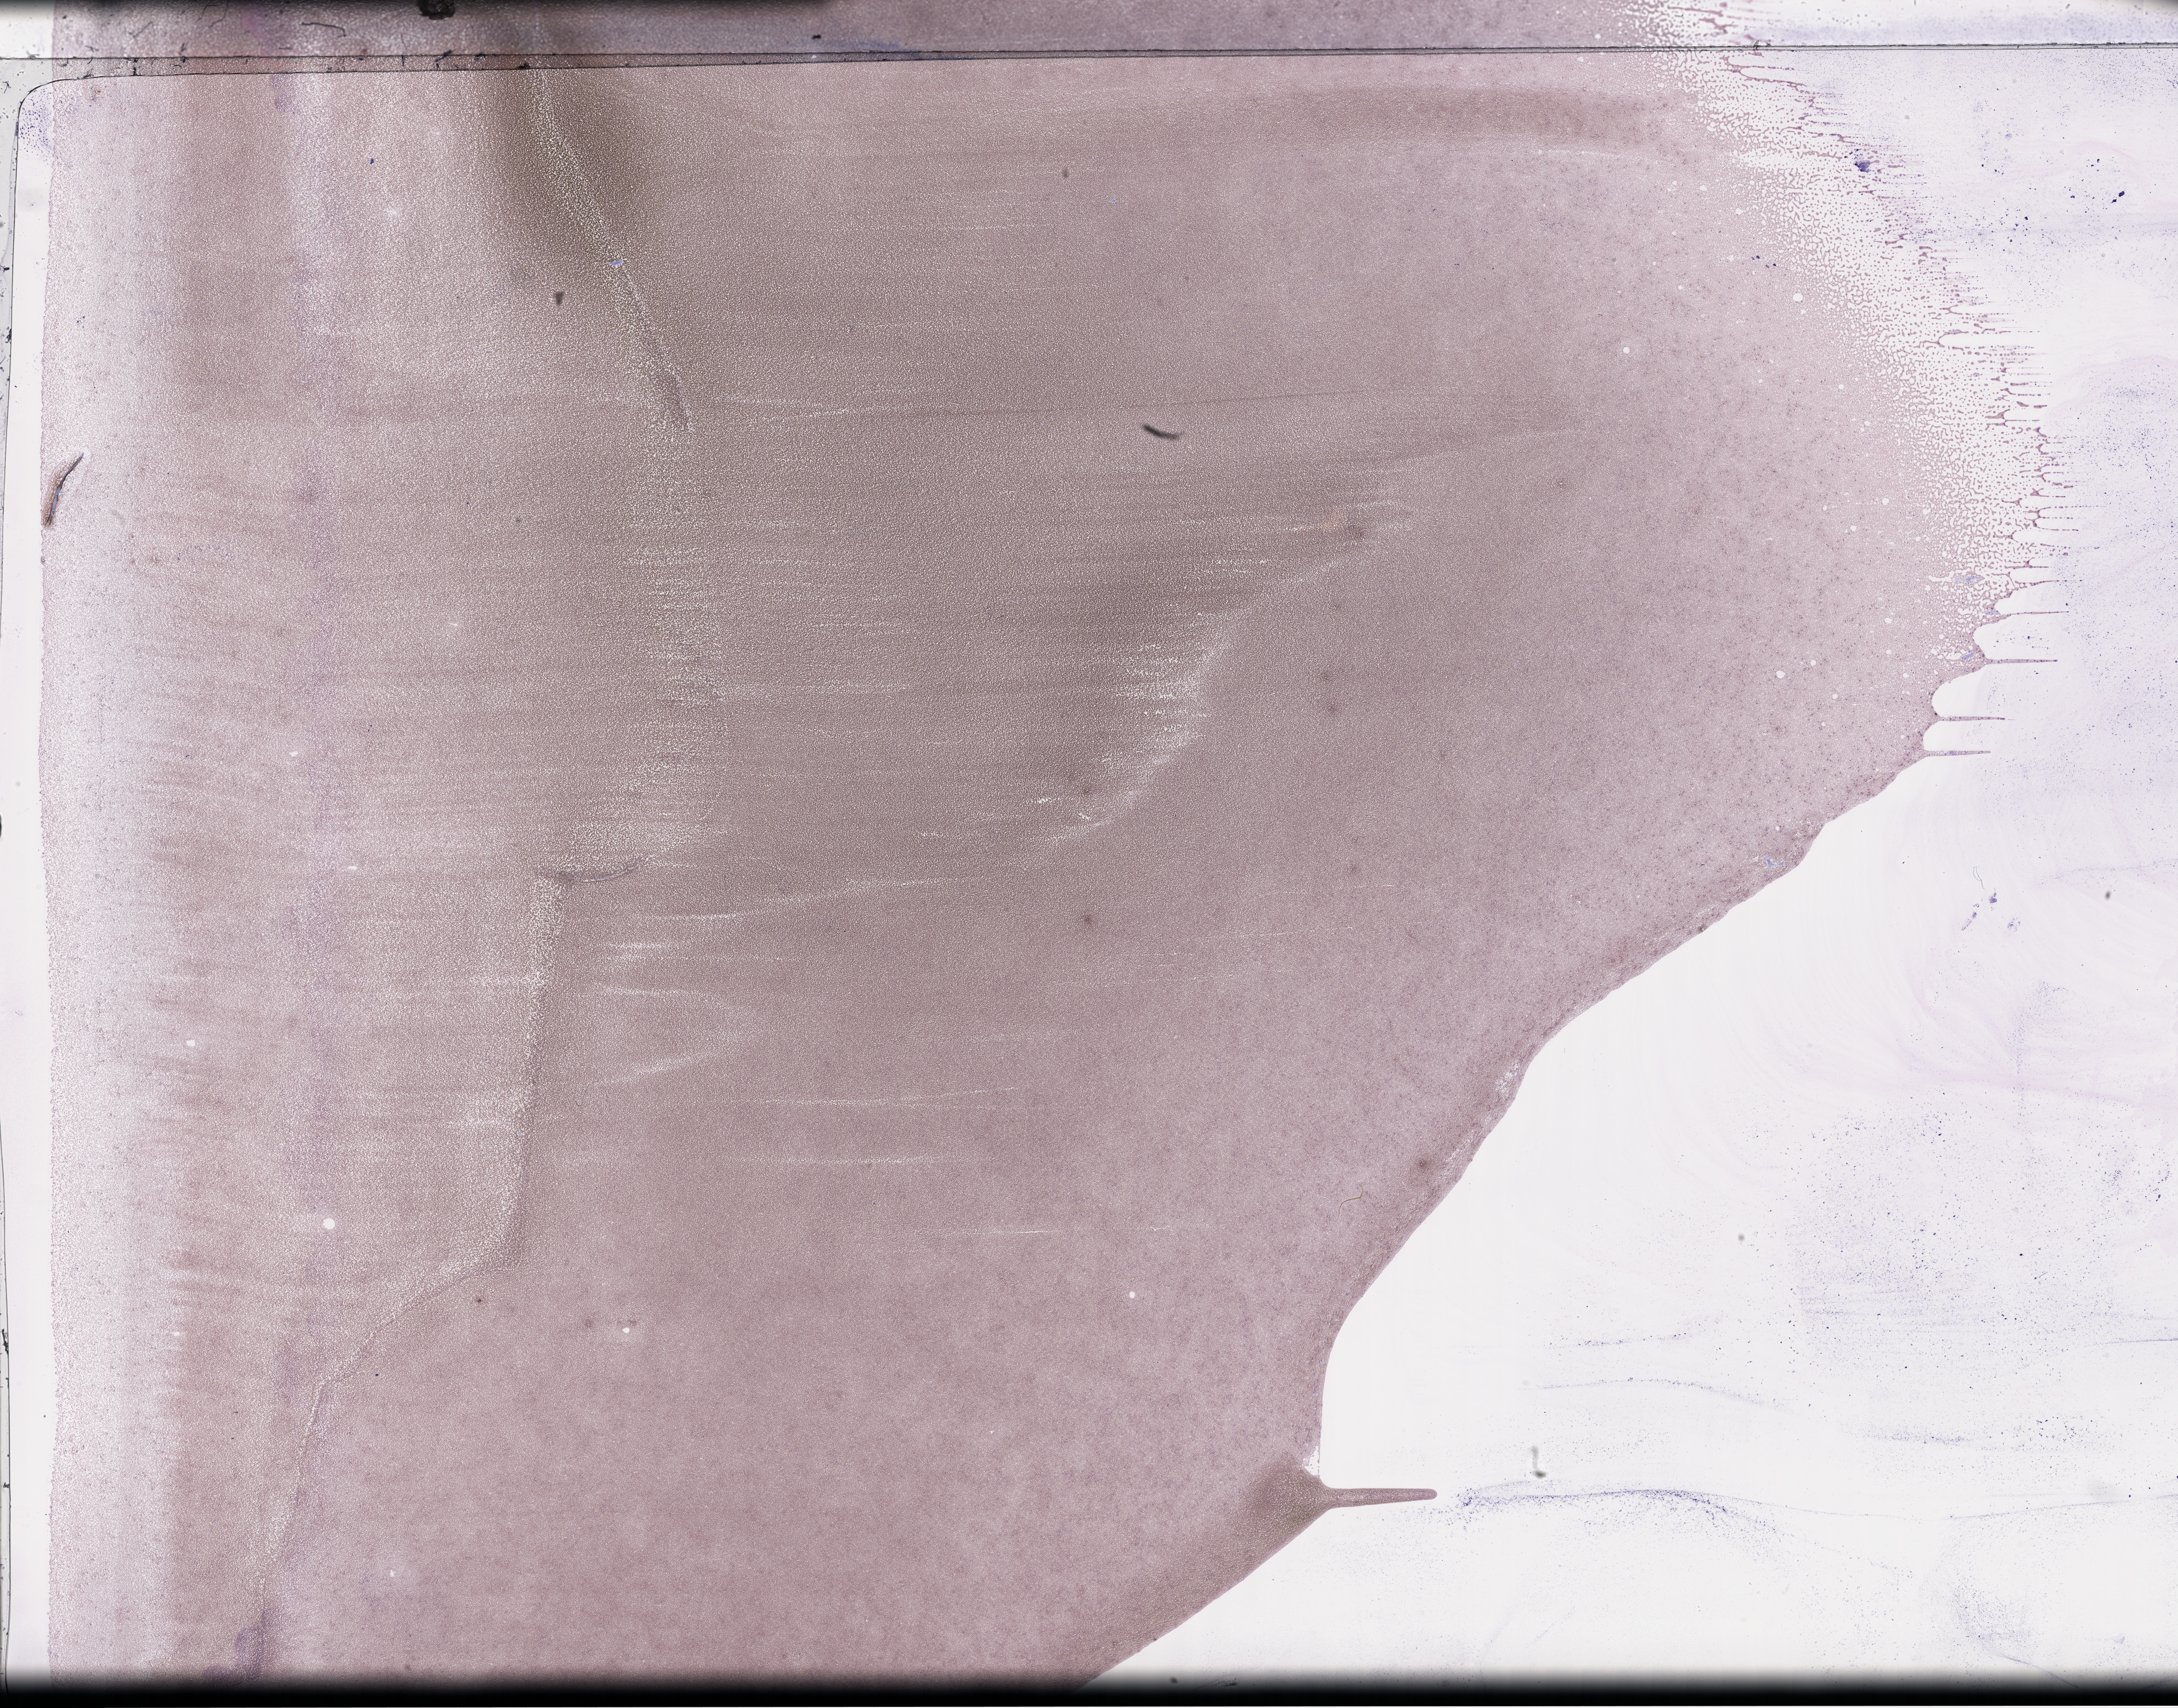
Whole-slide image of a whole blood smear, Wright–Giemsa stain — low-resolution overview of the scanned area, about 31.2 x 24.4 mm; EDTA-anticoagulated smear. Female patient.
- from a patient with: Plasma Cell Myeloma